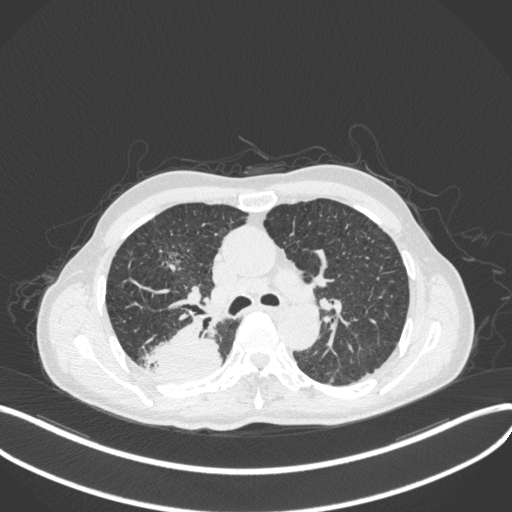
Chest CT, one axial slice; position 295 of 423 along the scan axis; lung window (W 1500 / L -600 HU); 1 mm slice thickness; 512 × 512 image matrix, field of view 400 × 400 mm. Patient: male, 79 years. Case-level facts recorded for this patient, not image findings: clinical TNM (as recorded): T3 N0 M0.
Annotated regions visible in this slice (bounding box drawn by a radiologist):
- lung tumour (recorded histology: adenocarcinoma): bounding box (x1, y1, x2, y2) in pixels: (143, 314, 224, 381)